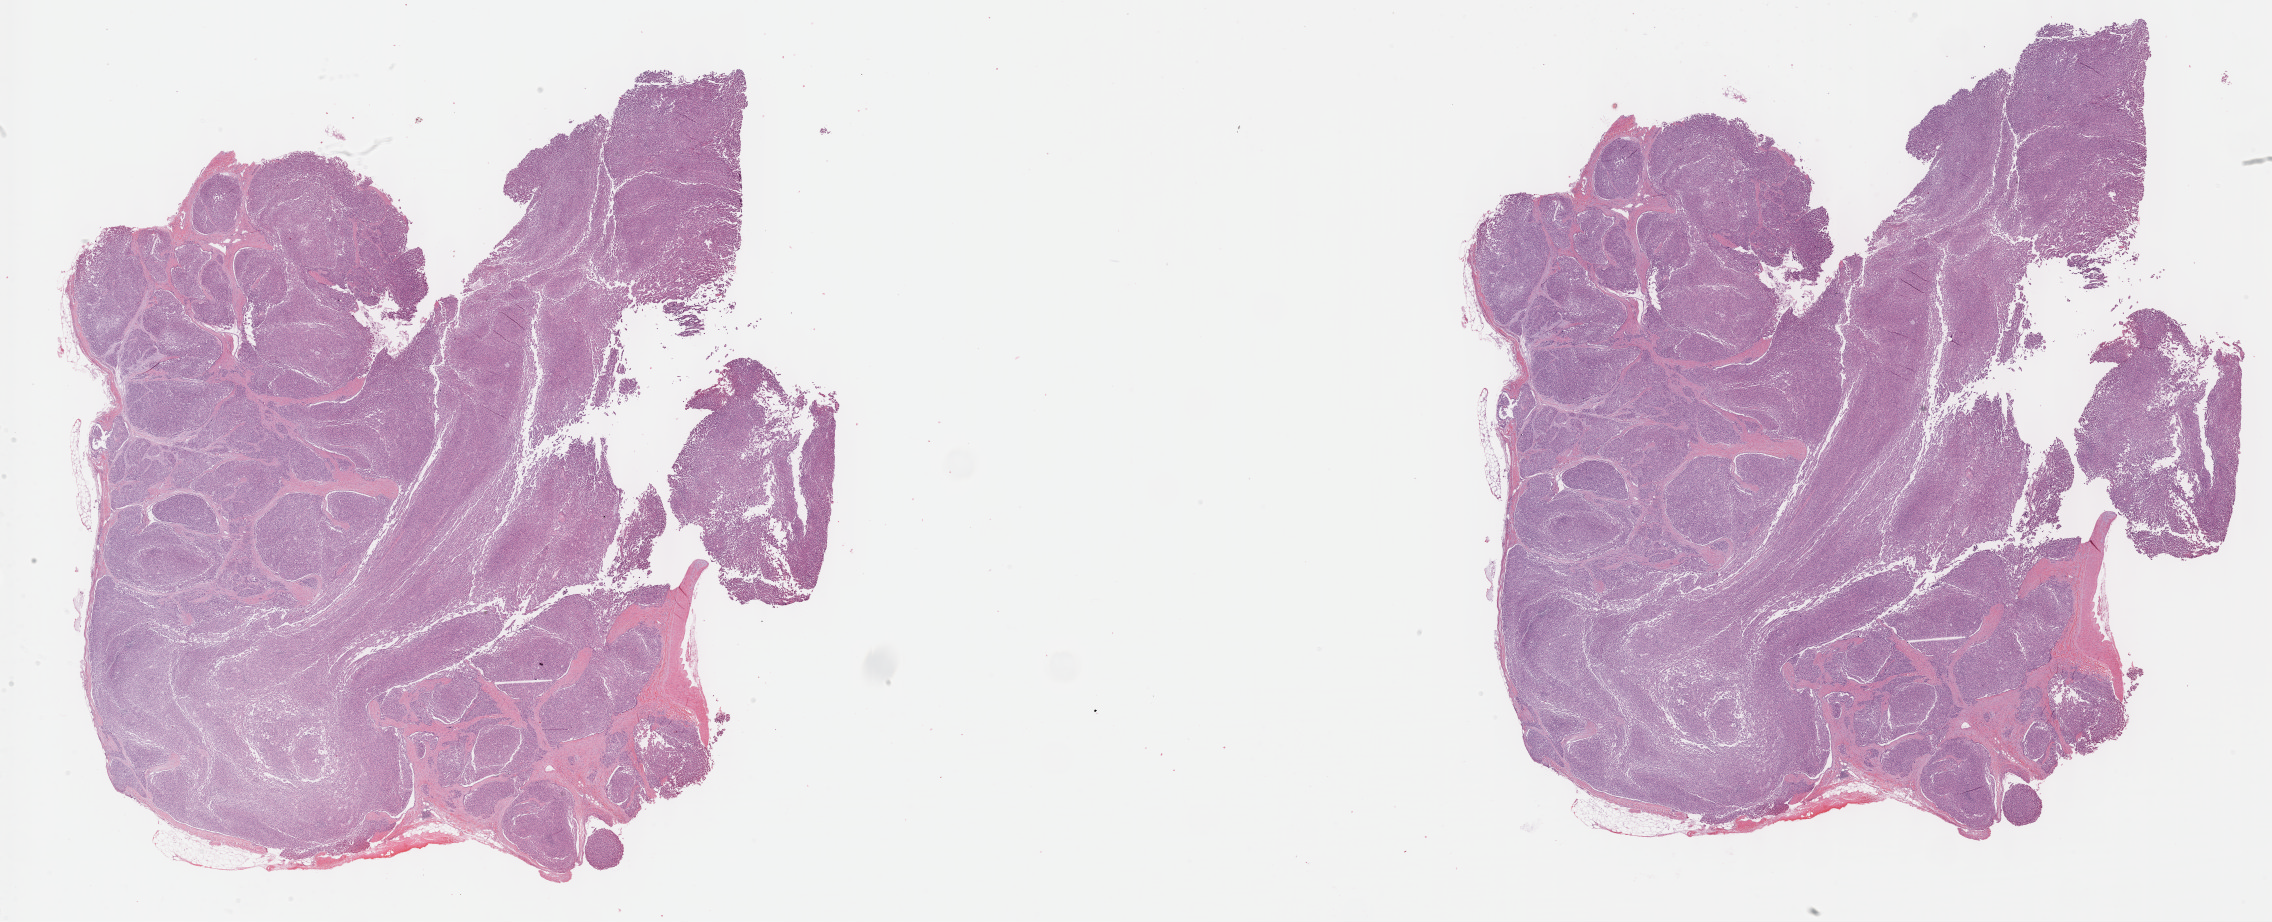
Digitized H&E tissue section (whole slide) — low-resolution overview of the scanned area, about 36.7 x 14.9 mm (slide scanned at 40x). FFPE section. Sample: primary tumour, kidney. Patient: male, age at initial diagnosis 48 years.
Pathologic diagnosis: Papillary adenocarcinoma, NOS. TNM: T1 NX M0. AJCC pathologic stage: I (7th edition).